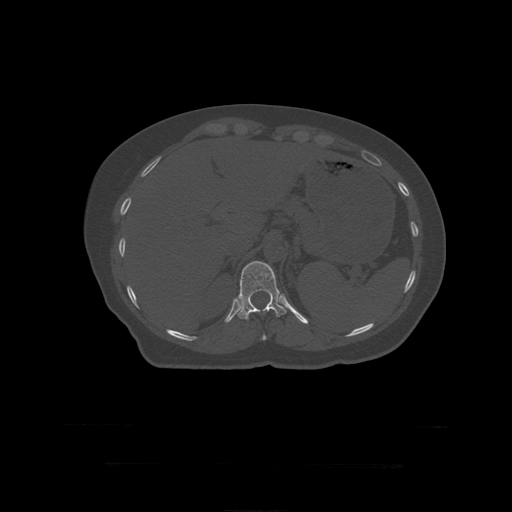
CT including the spine, one axial slice. Position 203 of 399 along the scan axis. 120 kVp. Bone window (W 1800 / L 400 HU). 512 × 512 image matrix, field of view 450 × 450 mm. Patient age 41 years. Case-level facts recorded for this patient, not image findings: primary cancer: breast.
Outlined on this slice (semi-automatic segmentation, software-assisted and operator-edited):
- T11 vertebra: box from (x=262, y=334) to (x=267, y=341) px
- T12 vertebra: (x=237, y=261)–(x=287, y=320)